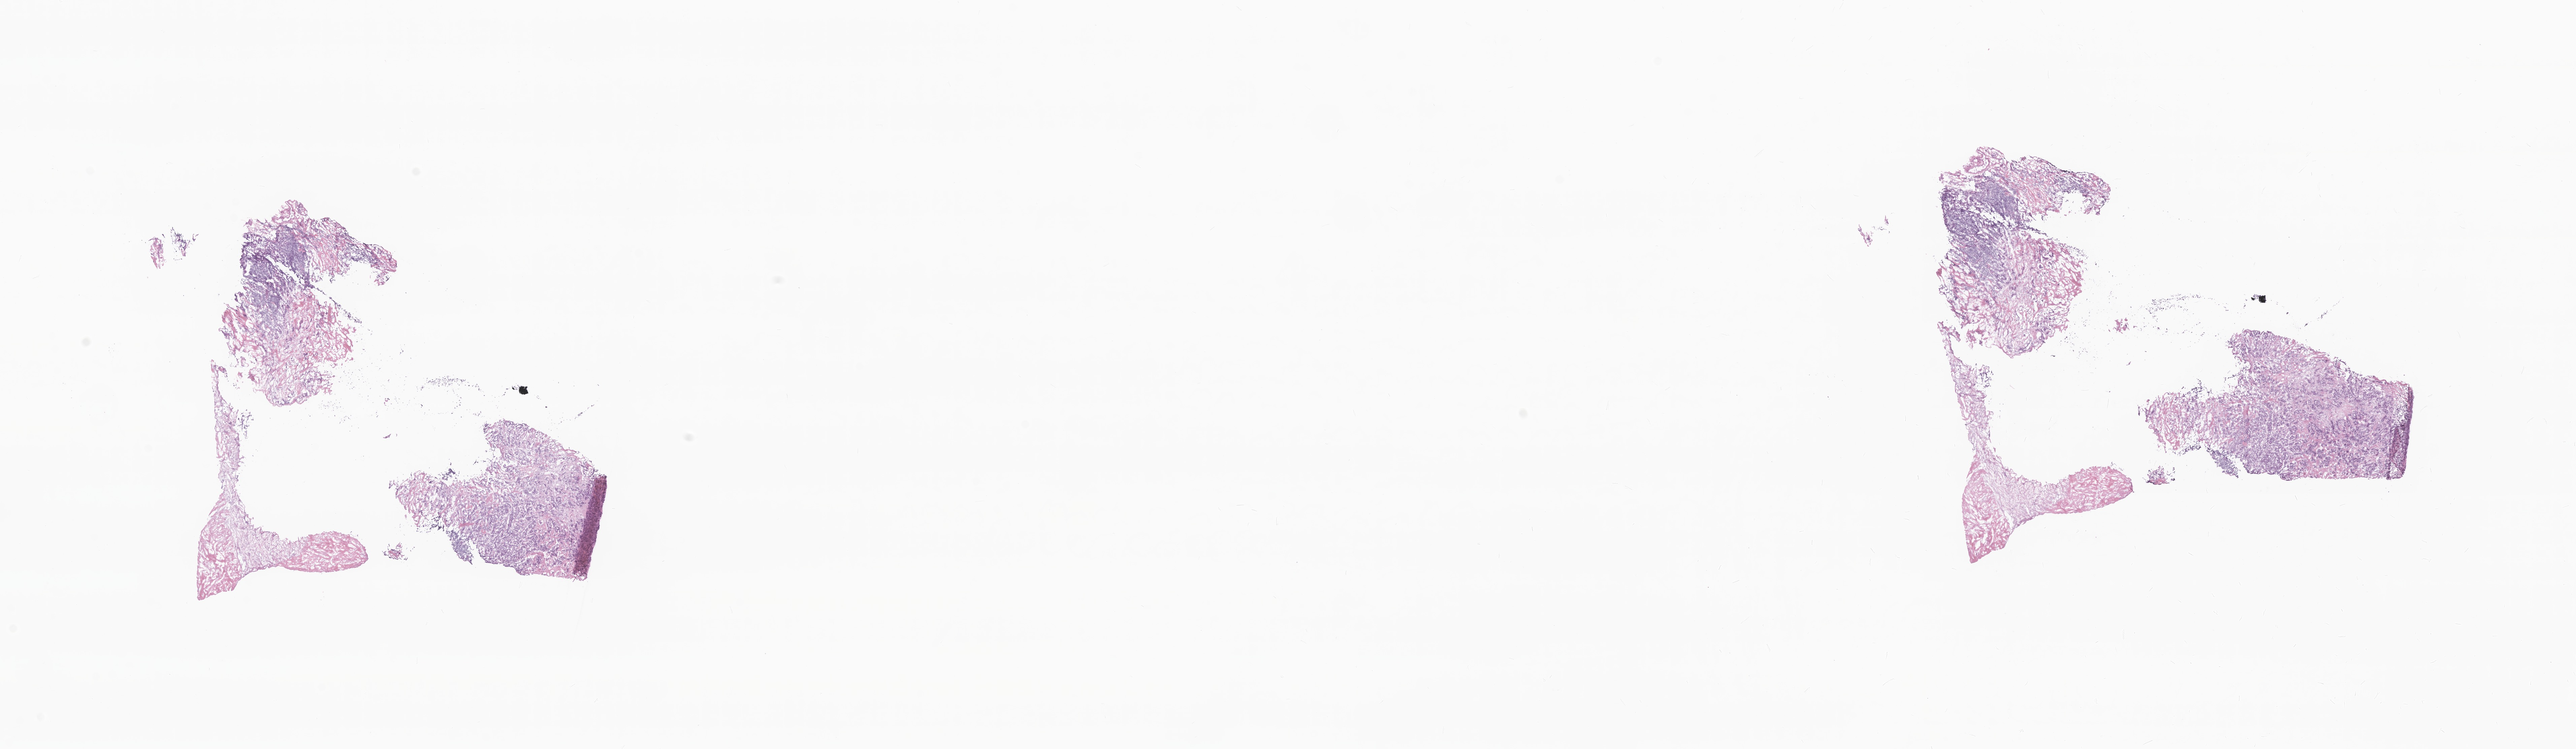
Whole-slide image, hematoxylin and eosin (H&E) stain — low-resolution overview of the scanned area, about 32.2 x 9.4 mm. Frozen section (tissue freezing medium). Primary tumor. Site: breast. Female patient; age at initial diagnosis 51 years. Composition of this section per pathologist review: tumor cells 60%, tumor nuclei 80%, stromal cells 30%, necrosis 10%, normal cells 0%. Infiltration values recorded for this section: lymphocyte infiltration 80%, monocyte infiltration 20%, neutrophil infiltration 0%.
Section: bottom of the tissue portion. Histologic diagnosis: Infiltrating duct carcinoma, NOS.